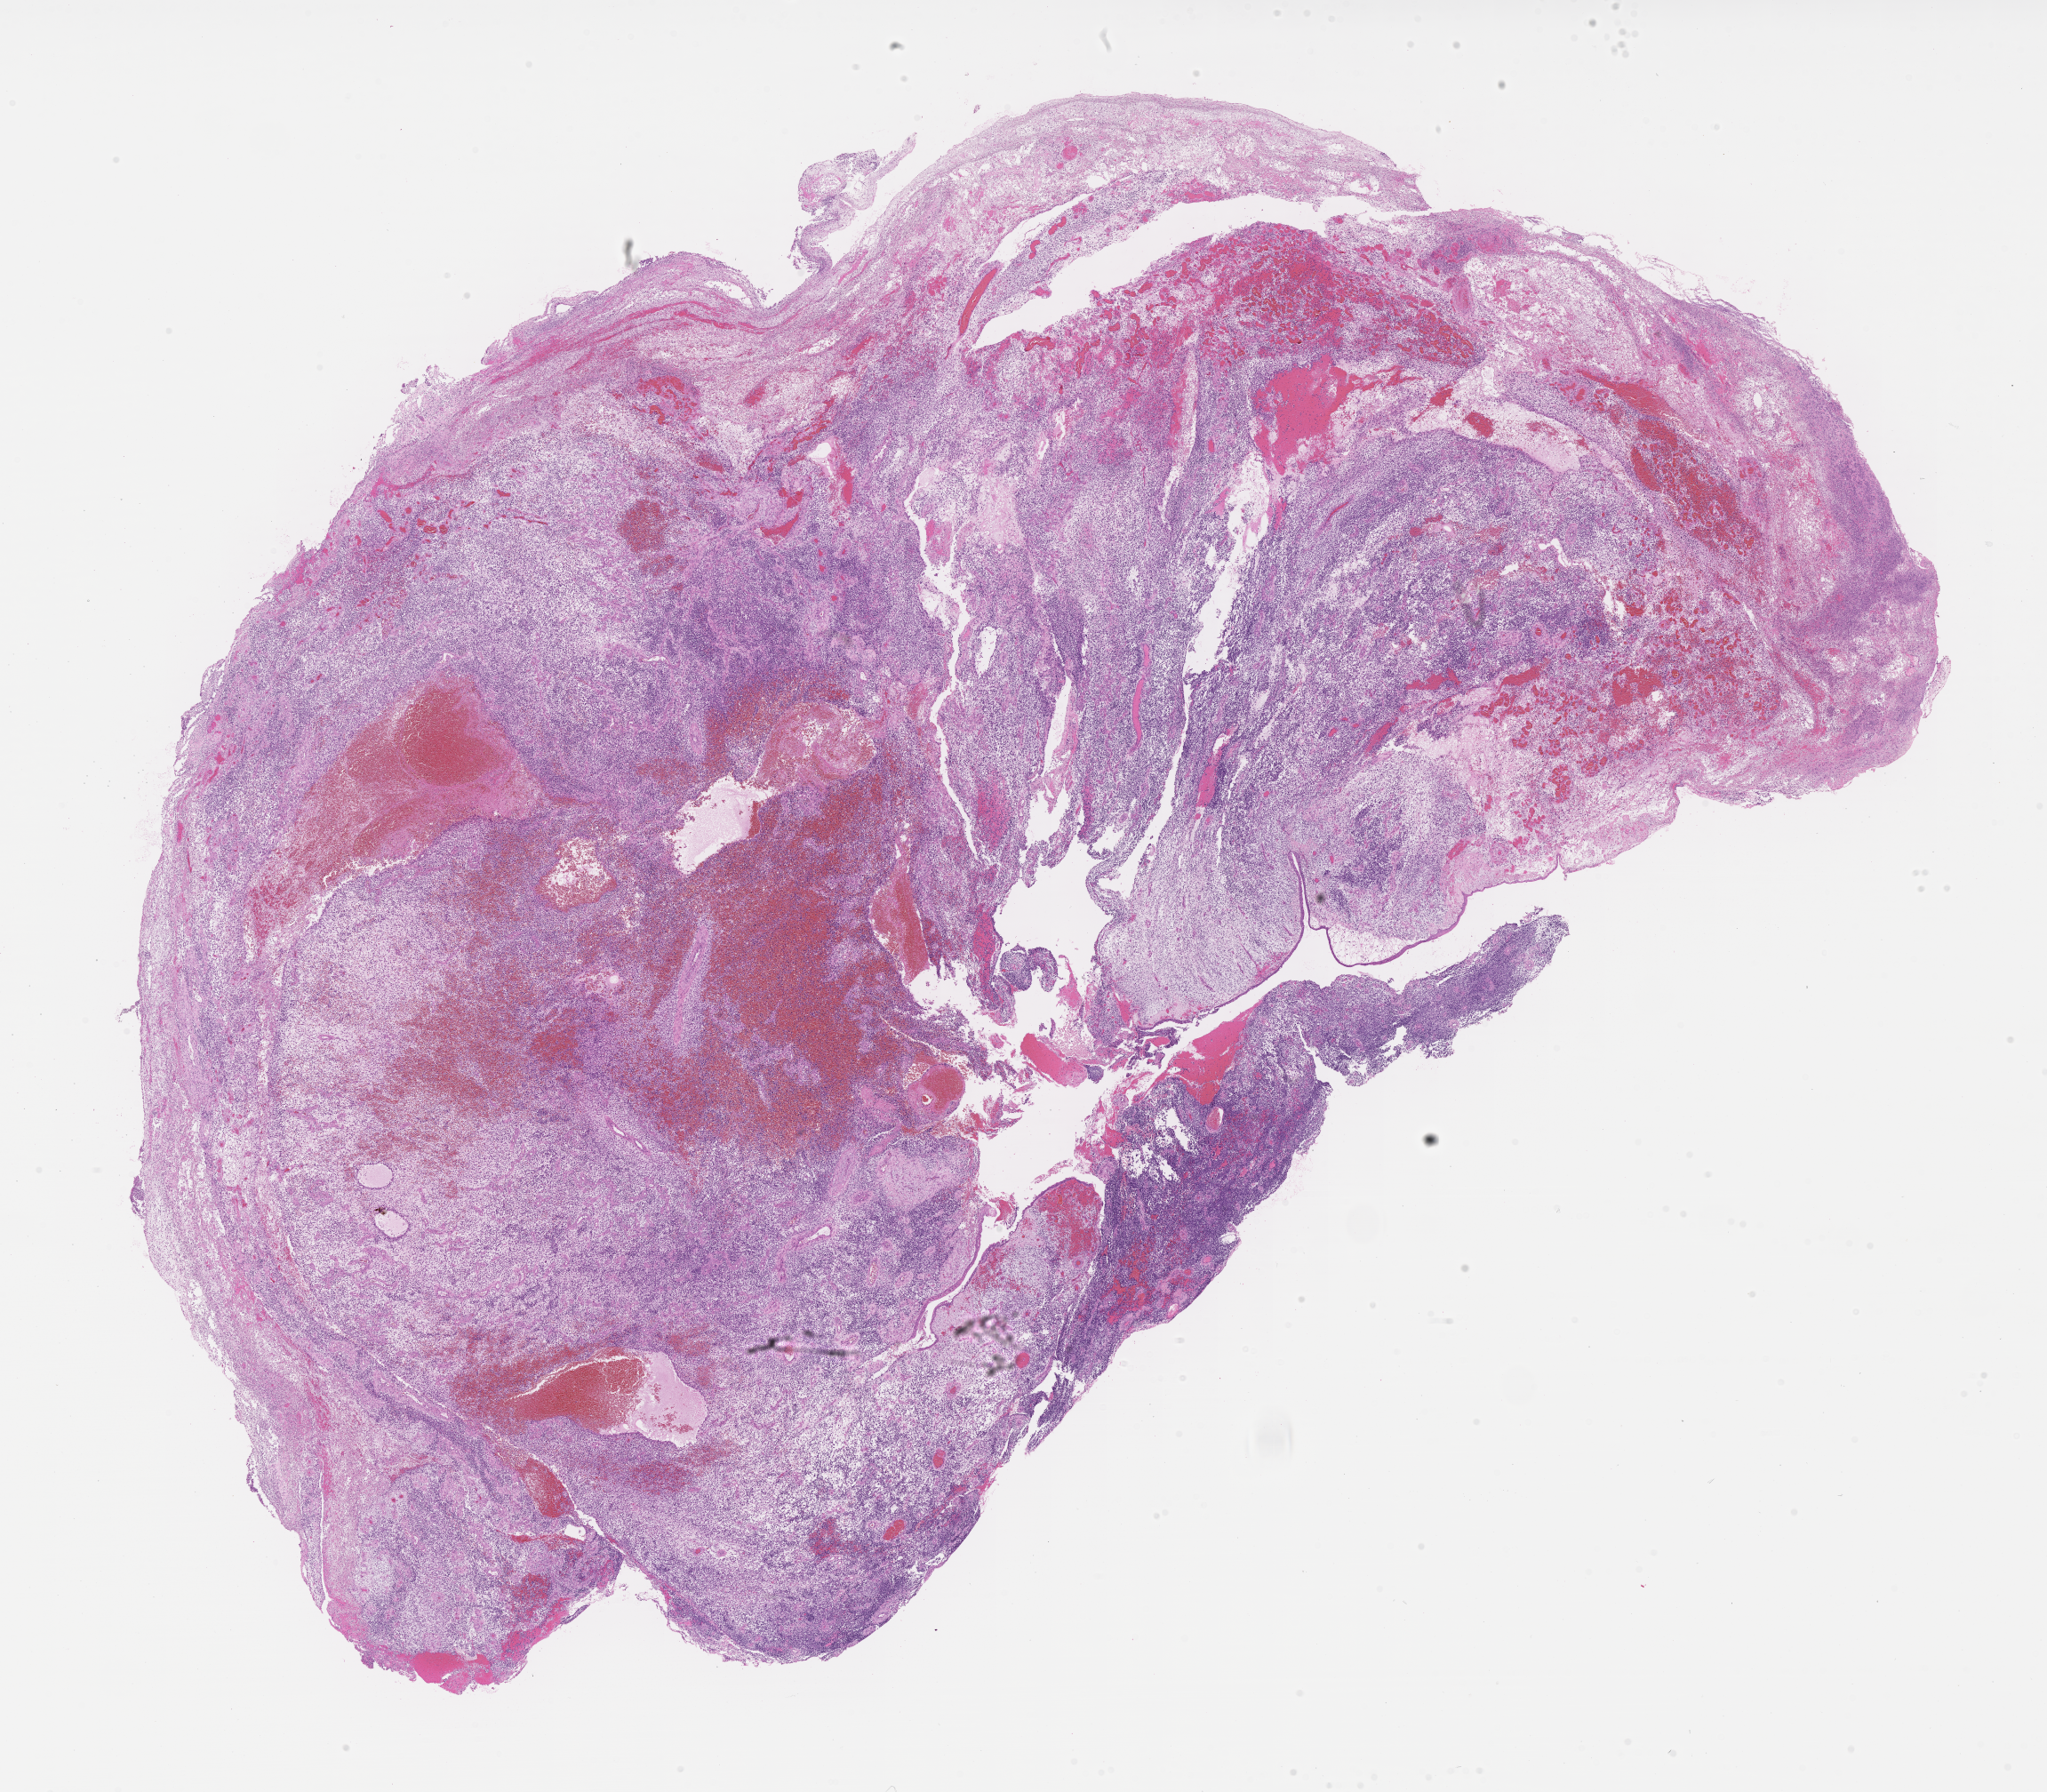
Whole-slide image, hematoxylin and eosin (H&E) stain of tumor tissue, shown as a low-resolution overview of the whole scanned area (about 18.6 x 16.3 mm). FFPE section. Site: nasopharynx-left (nose). Male patient, age at diagnosis 6.6 years.
Diagnosis: rhabdomyosarcoma; histological classification: embryonal rhabdomyosarcoma. Stage (as recorded): 3.